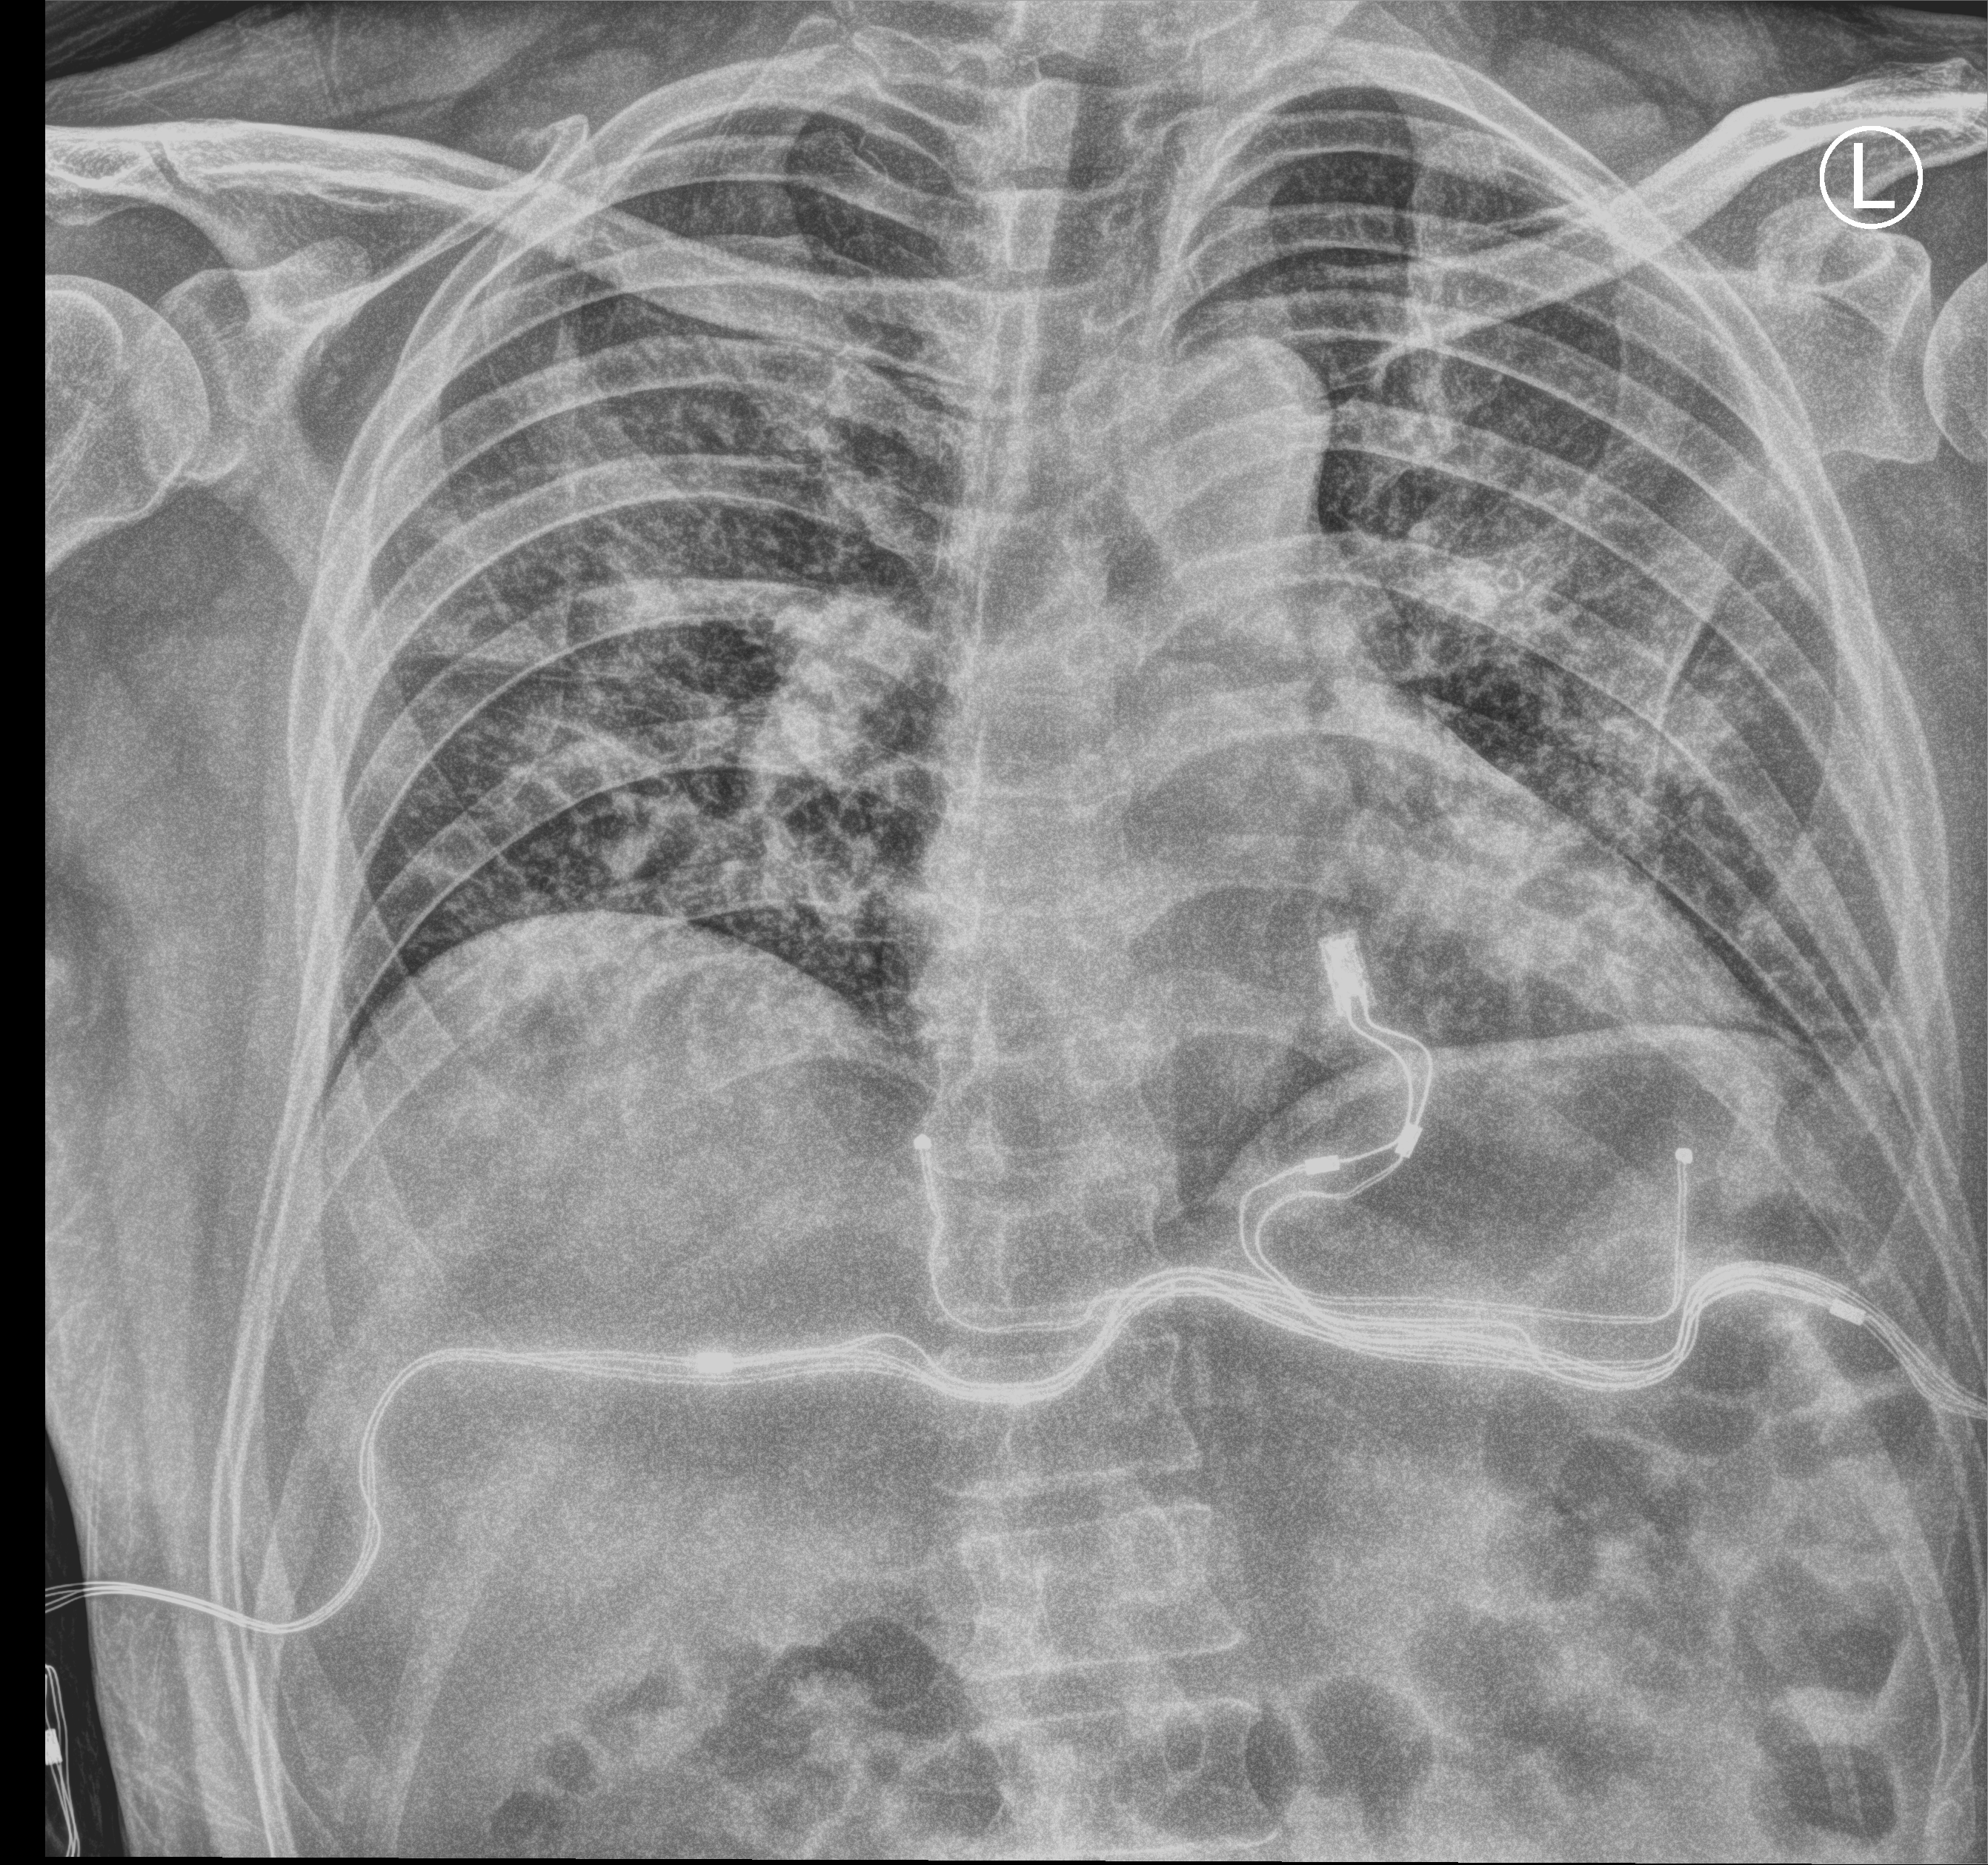
Portable chest radiograph, anteroposterior (AP) projection. Male patient hospitalised with COVID-19, age 18–59 years.
Hospital-stay facts (about this admission, not read from this image; timing relative to this image not recorded): hypertension (admission record): no; mechanically ventilated during this hospital stay: no.